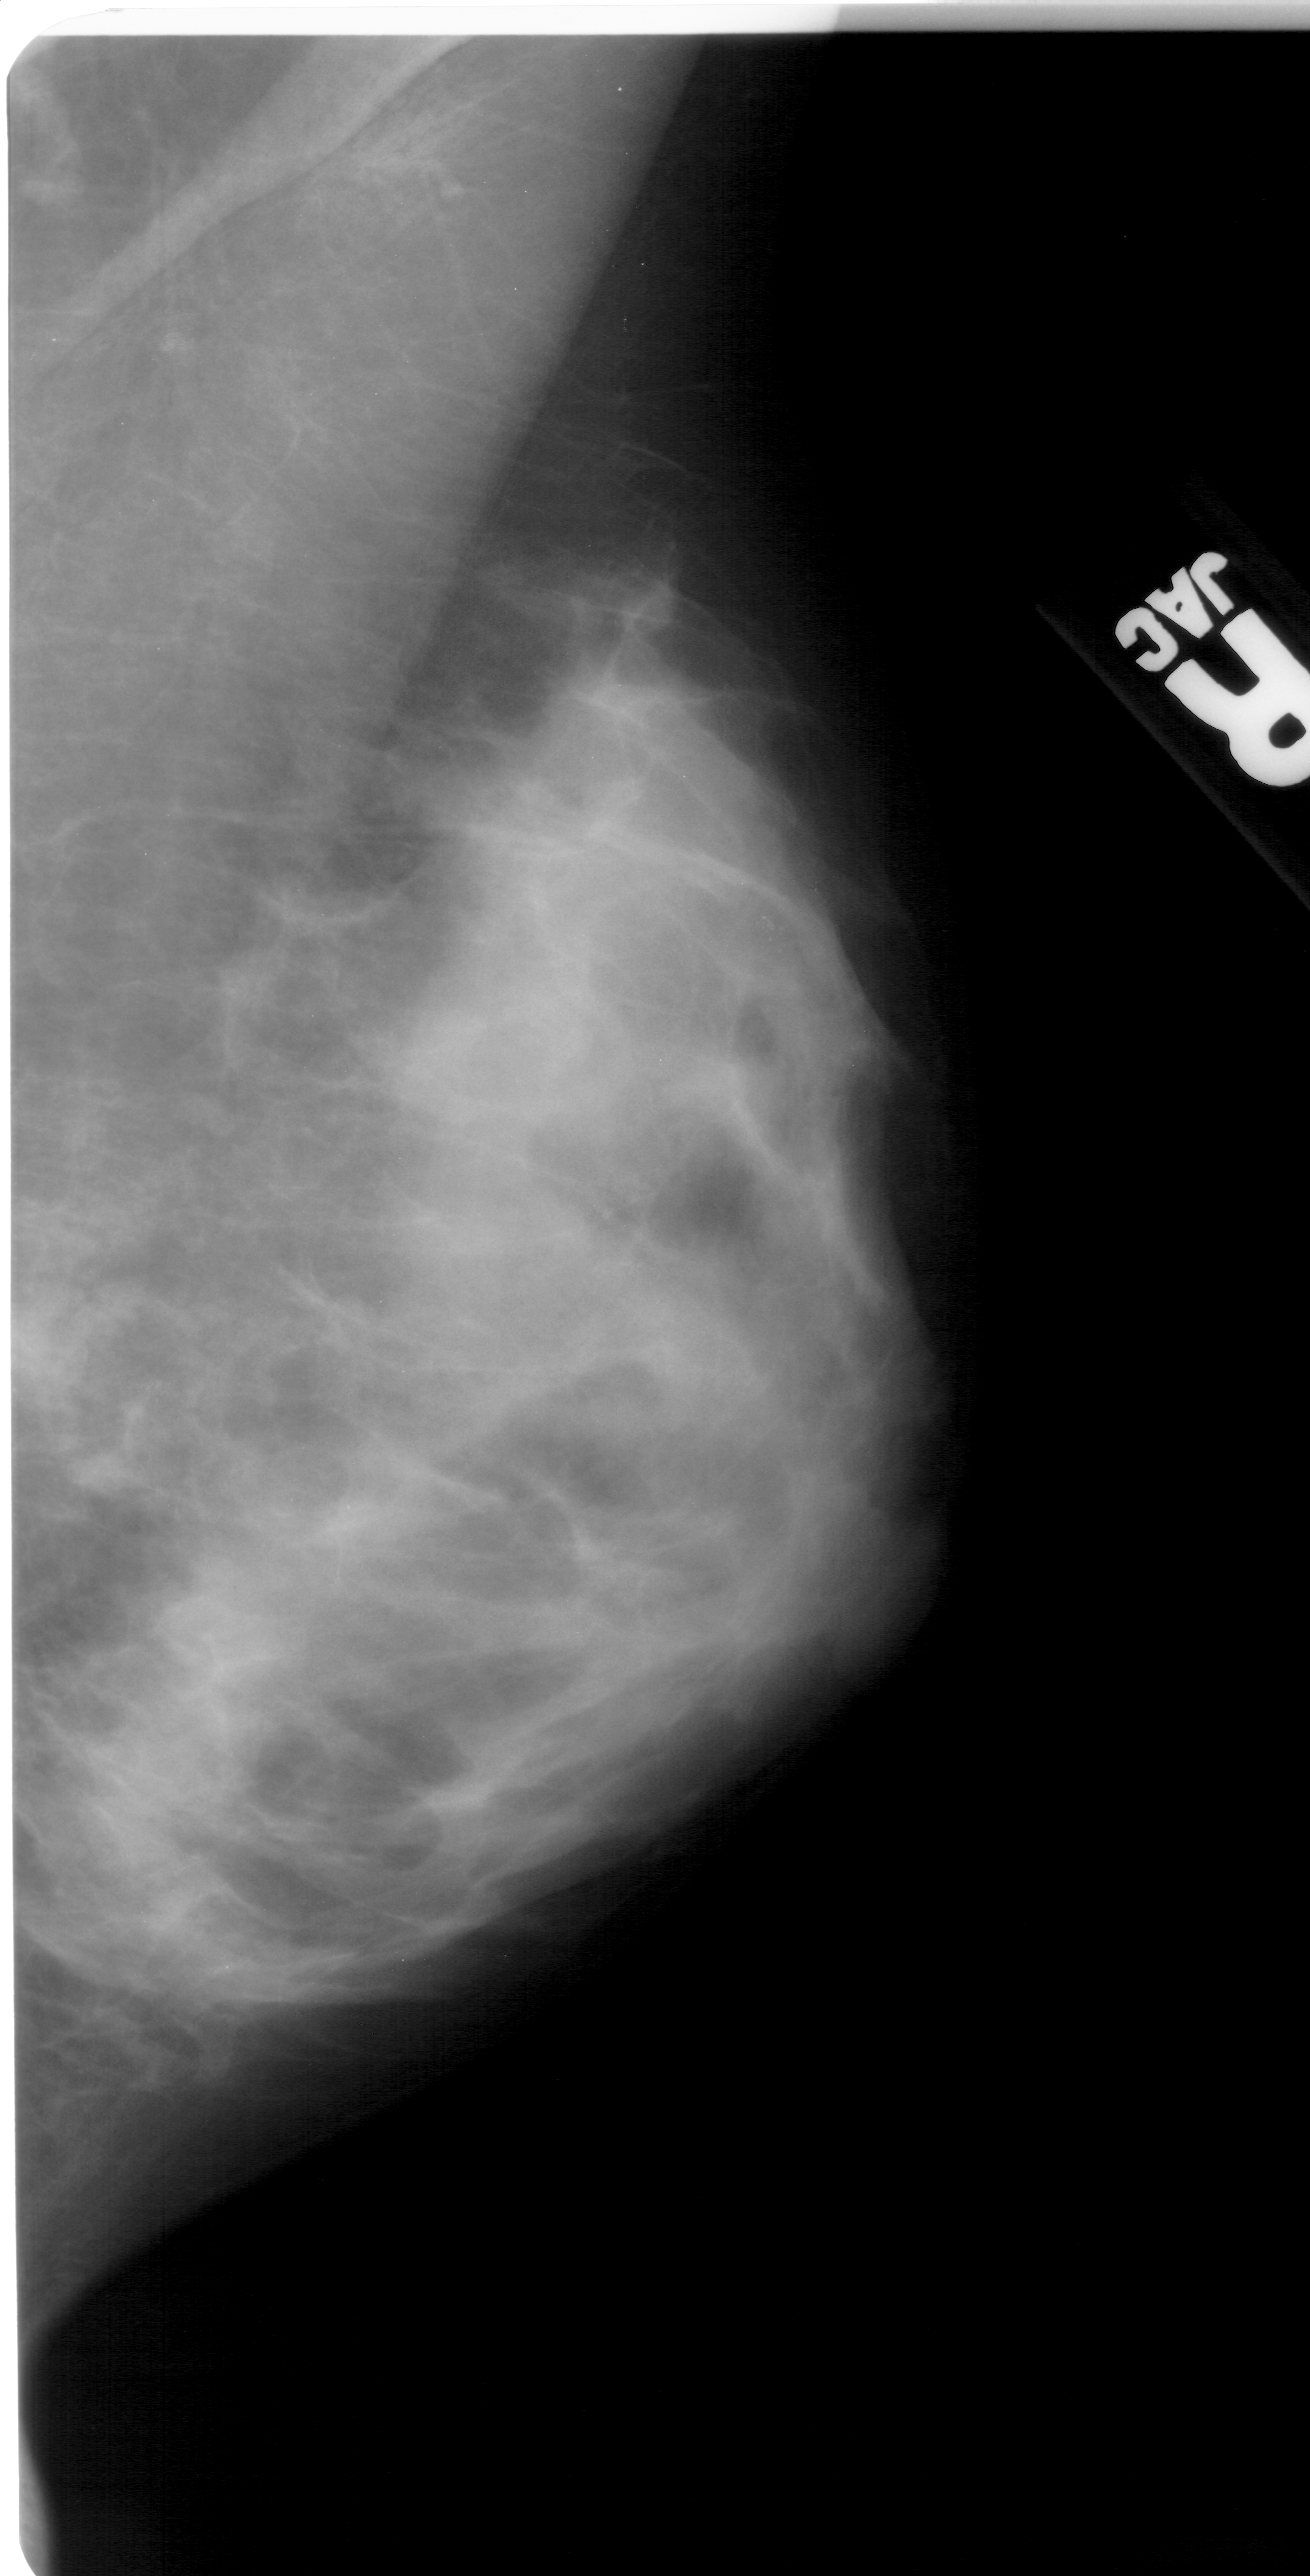
Scanned film-screen mammogram; right breast; mediolateral oblique (MLO) view; BI-RADS breast density category 4 (scale 1–4).
- Calcifications, morphology pleomorphic, distribution clustered; BI-RADS assessment category 4; pathology (as recorded): benign.